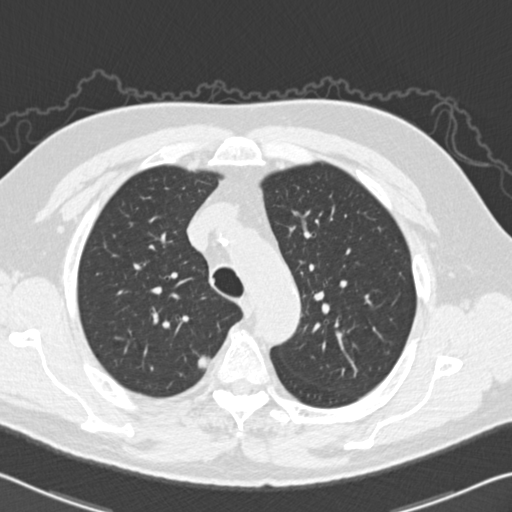
Low-dose screening chest CT, one axial slice; reconstruction kernel B30f; 120 kVp; lung window (W 1500 / L -600 HU); 2 mm slice thickness; 512 × 512 image matrix, field of view 340 × 340 mm.
Outlined on this slice (expert manual segmentation):
- lesion 1 (tumor, upper lobe of right lung): bounding box (x1, y1, x2, y2) in pixels: (198, 356, 210, 369)